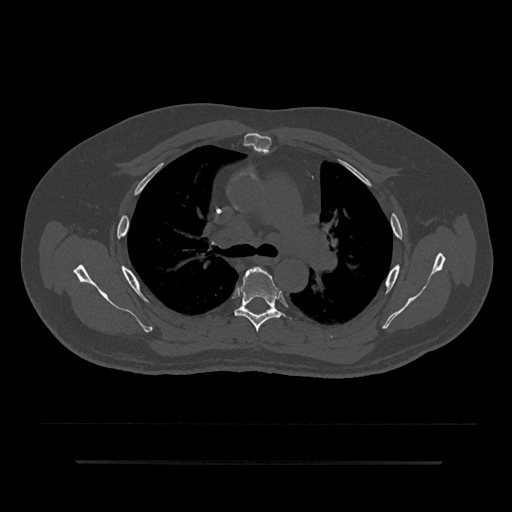
CT including the spine, one axial slice. Position 575 of 797 along the scan axis. Reconstruction kernel Br40s/3. 120 kVp. Bone window (W 1800 / L 400 HU). 0.5 mm slice thickness. 512 × 512 image matrix, field of view 464 × 464 mm. Patient: male, 59 years. From the clinical record (not read from this slice): primary cancer: bile ducts.
Structures marked on this image (semi-automatically segmented with operator editing):
- T4 vertebra: bounding box (x1, y1, x2, y2) in pixels: (253, 266, 258, 268)
- T5 vertebra: (234, 267, 282, 332)